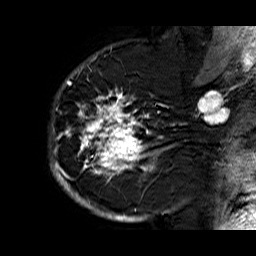
Breast MRI (dynamic contrast-enhanced), one sagittal slice; position 45 of 60 along the scan axis; dynamic contrast-enhanced series, time point 2 of 6 at this slice position (early post-contrast); 1.5 T; TE 6.3 ms, TR 32.9 ms; 4 mm slice thickness; 256 × 256 image matrix, field of view 200 × 200 mm. Female patient. From the clinical record (not read from this slice): setting: breast cancer imaged before/during neoadjuvant chemotherapy; receptor status: HR-positive, HER2-negative.
Annotated regions visible in this slice (semi-automatic segmentation, software-assisted and operator-edited):
- analysis volume of interest (the breast-tissue region the enhancement analysis was run in; not a lesion): box from (x=49, y=74) to (x=176, y=210) px
- tumour enhancement mask (voxels above the 100 % enhancement threshold inside the analysis volume of interest): (x=50, y=74)–(x=172, y=210)